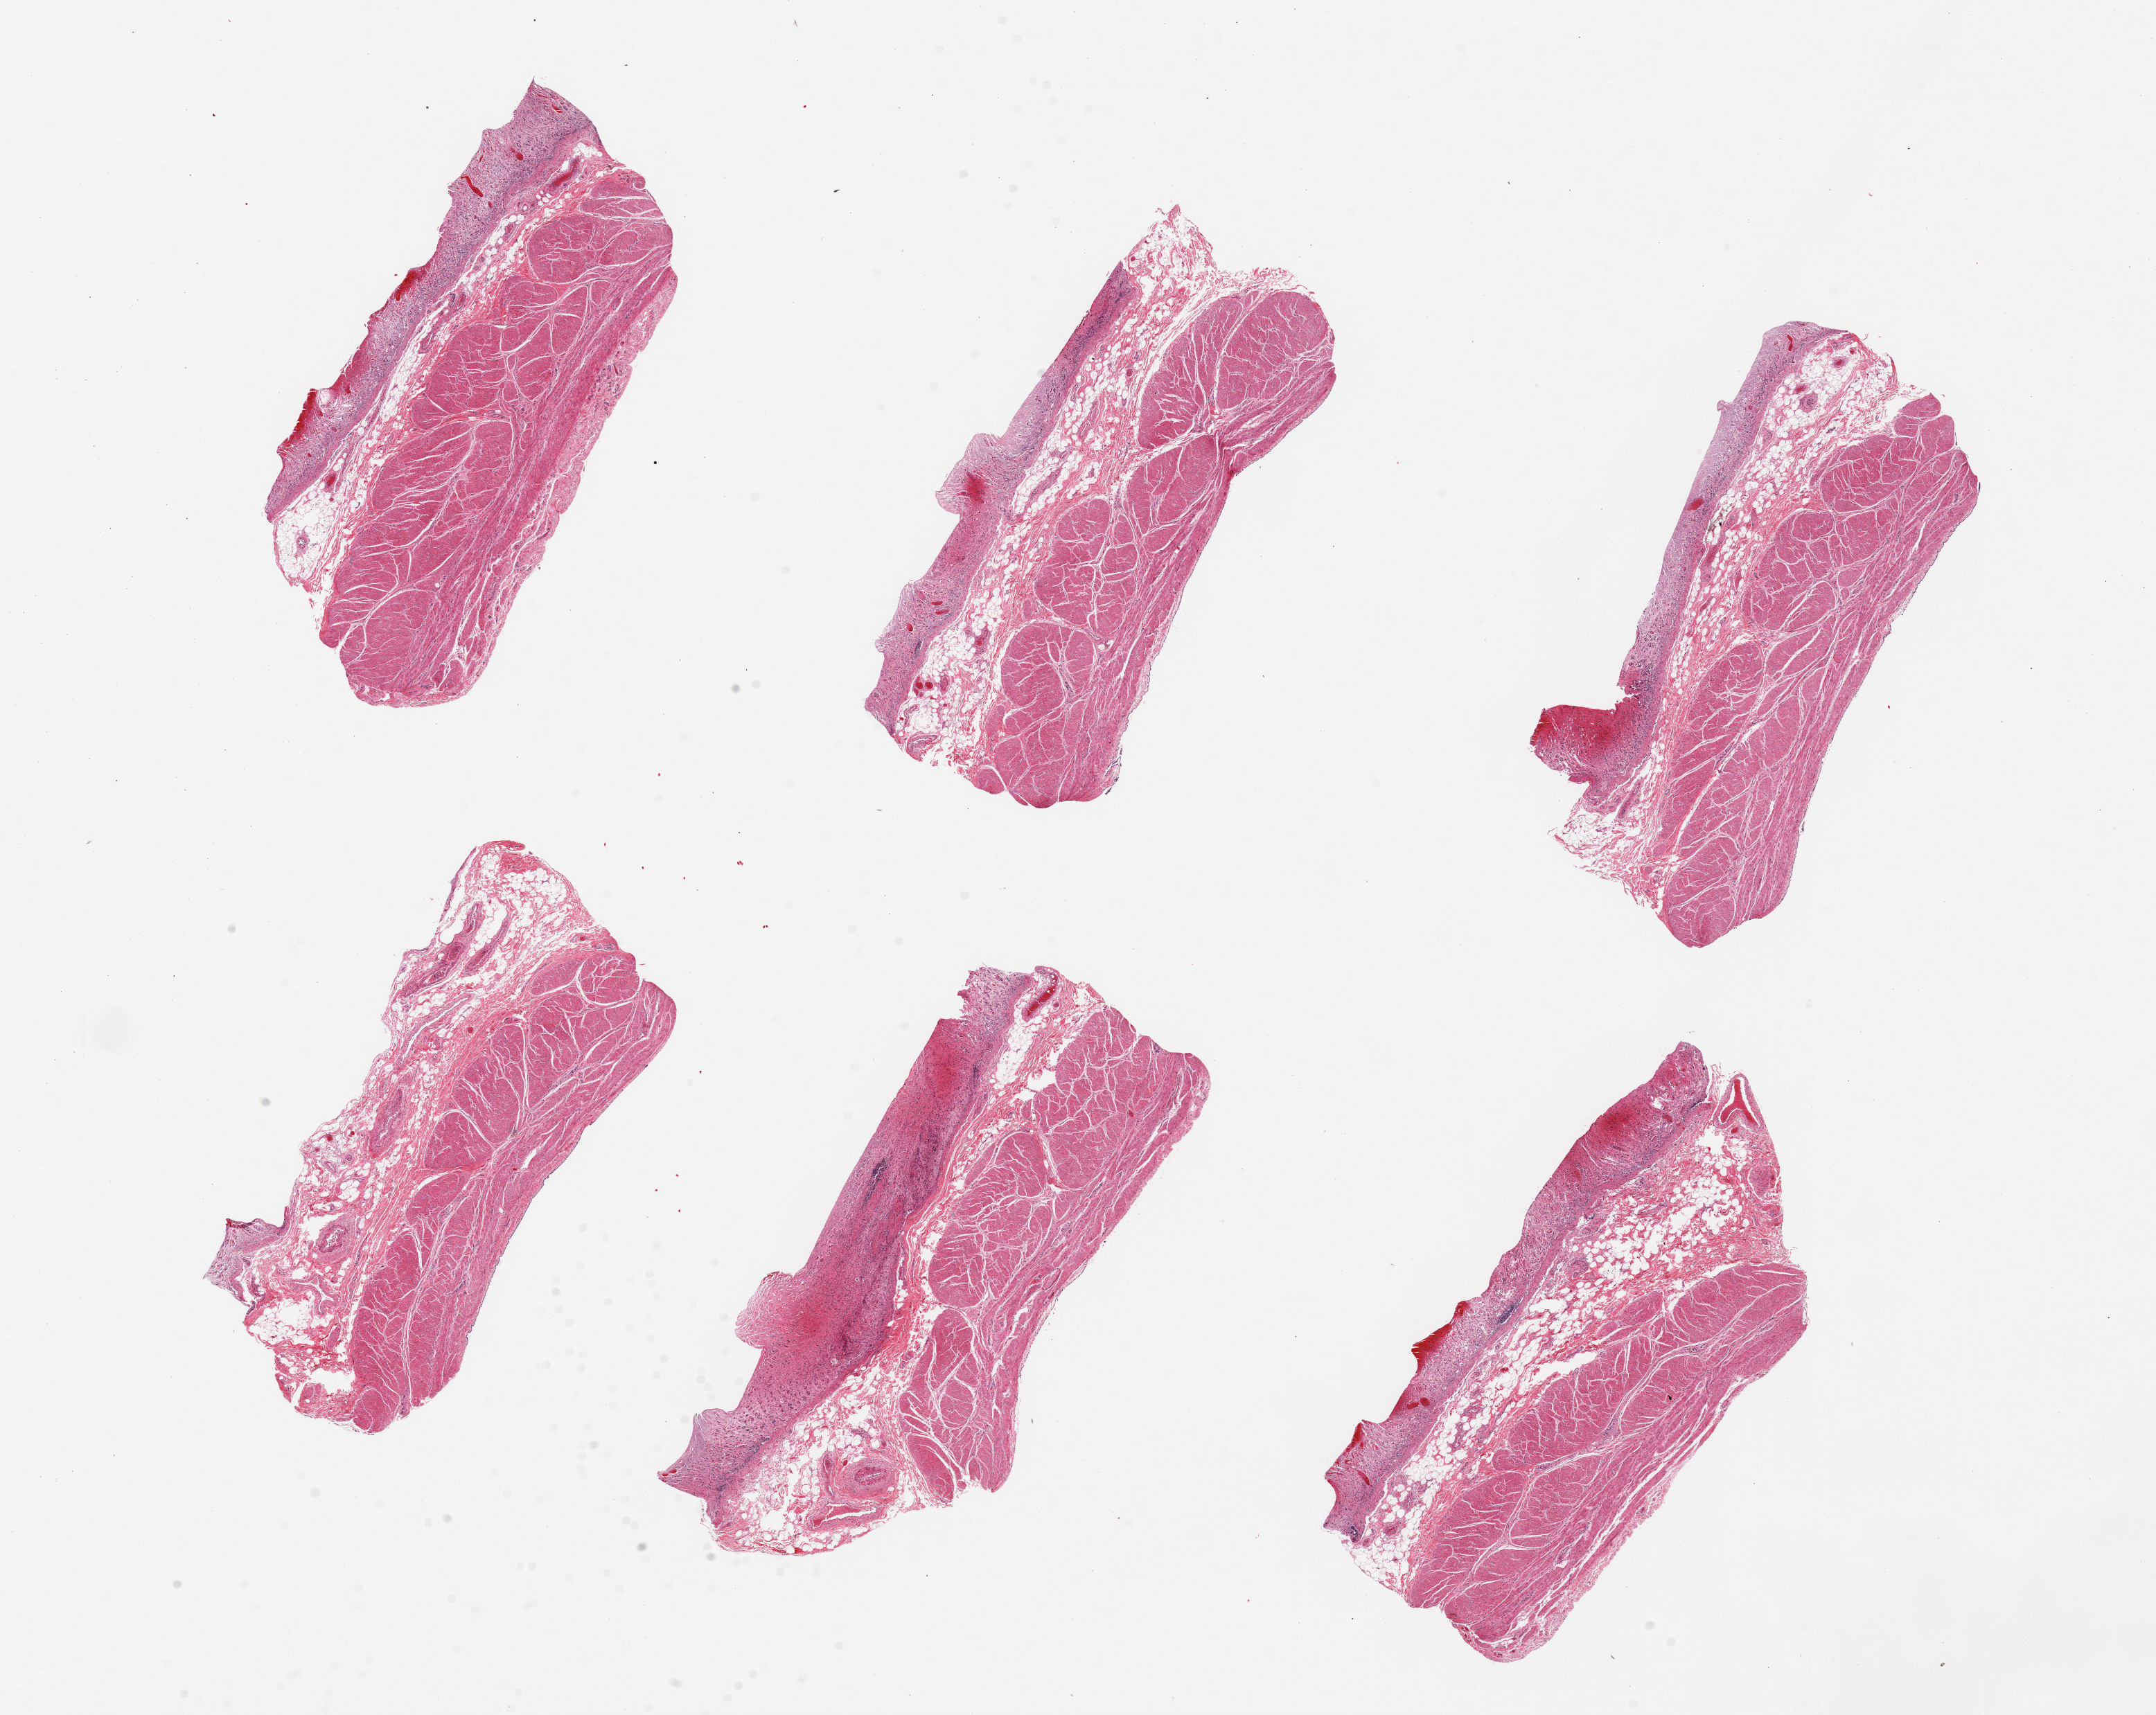
Whole-slide image, hematoxylin and eosin (H&E) stain, whole scanned area (about 24.6 x 19.6 mm) shown as a low-resolution overview, PAXgene-fixed paraffin-embedded (PFPE) section, sampled site (target tissue): stomach, tissue donor sample. Female donor.
Pathologist's review note for this sample: 6 pieces, up to 8x3mm; Mucosa=3; muscle = 2. Mucosal hemorrhage.